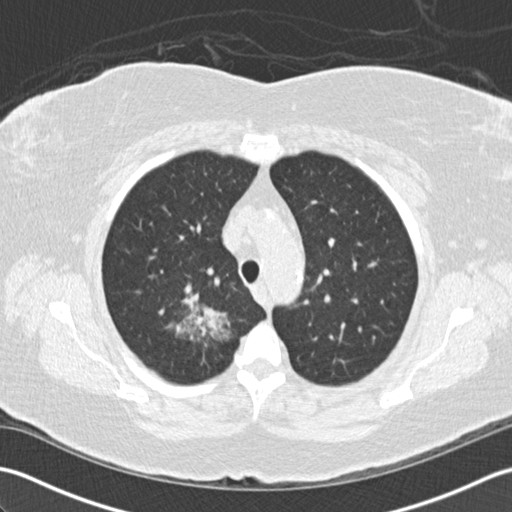
Low-dose screening chest CT, axial slice, baseline screening round, lung window (W 1500 / L -600 HU), 120 kVp. Female, age 72 years at enrolment.
Expert-annotated lung lesion, bounding box (x1, y1, x2, y2) in pixels: (138, 274, 237, 369). The screening reader recorded 2 non-calcified nodules or masses ≥4 mm on this exam (right lower lobe, right lower lobe); which of them this box marks is not recorded. Official screen result: positive, change unspecified: nodule(s) >= 4 mm or enlarging nodule(s), mass(es), or other non-specific abnormalities suspicious for lung cancer. Later outcome: lung cancer diagnosed 494 days after this screen (after the second annual screen) — bronchiolo-alveolar adenocarcinoma, NOS, right upper lobe, stage IIIB (AJCC 6th edition), 45 mm at pathology.